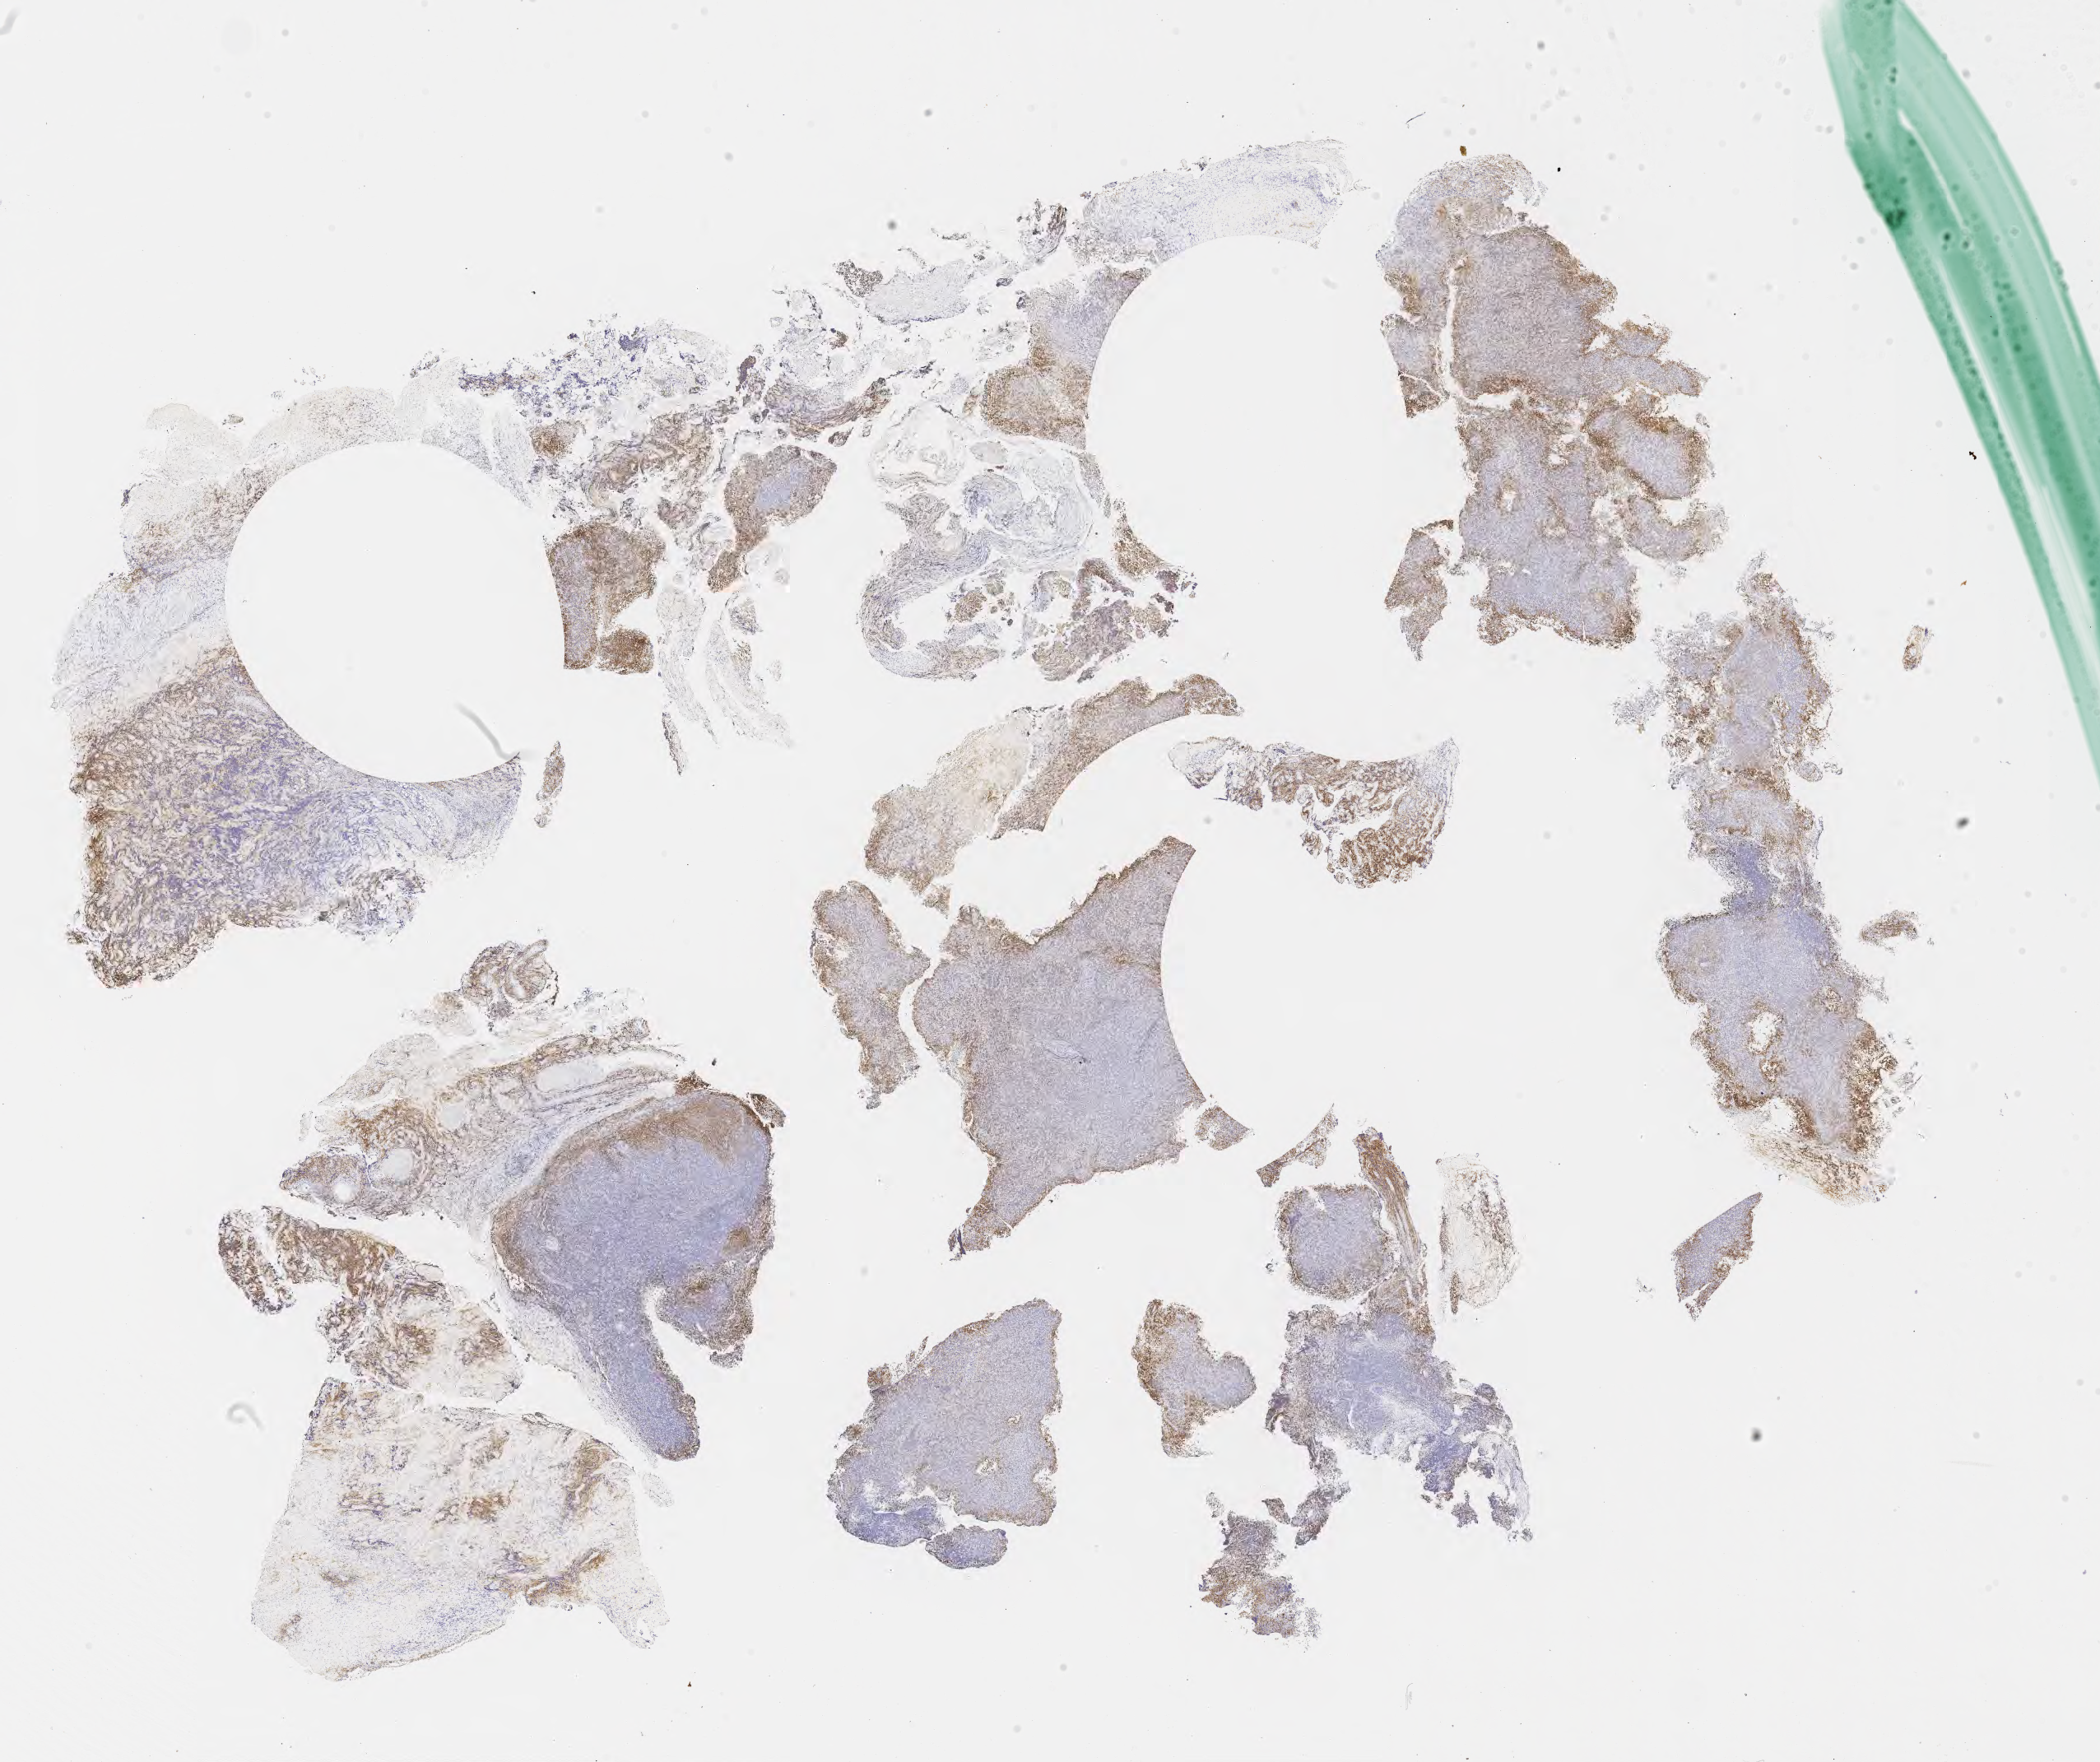
IHC for CD20, whole-slide image — whole scanned area (about 20.6 x 17.3 mm) shown as a low-resolution overview; tumor tissue; site: lymph node. Patient: male, 29 years old.
Diagnosis: Diffuse large B-cell lymphoma, NOS.